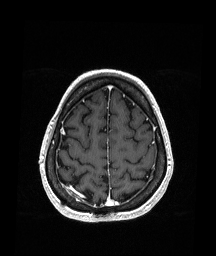
Brain MRI from a brain-tumour surgery series, one axial slice. Slice 52 of 151 in the series (ordered by position). T1-weighted post-contrast. 1.05 mm slice thickness. 216 × 256 image matrix, field of view 211 × 250 mm. From the clinical record (not read from this slice): histopathology: Oligodendroglioma; WHO grade: 2; IDH mutation: yes; tumour location: Right Parietal.
Annotated regions visible in this slice (expert manual segmentation):
- previous resection cavity: bounding box <95,174,102,181> (left, top, right, bottom; pixels)